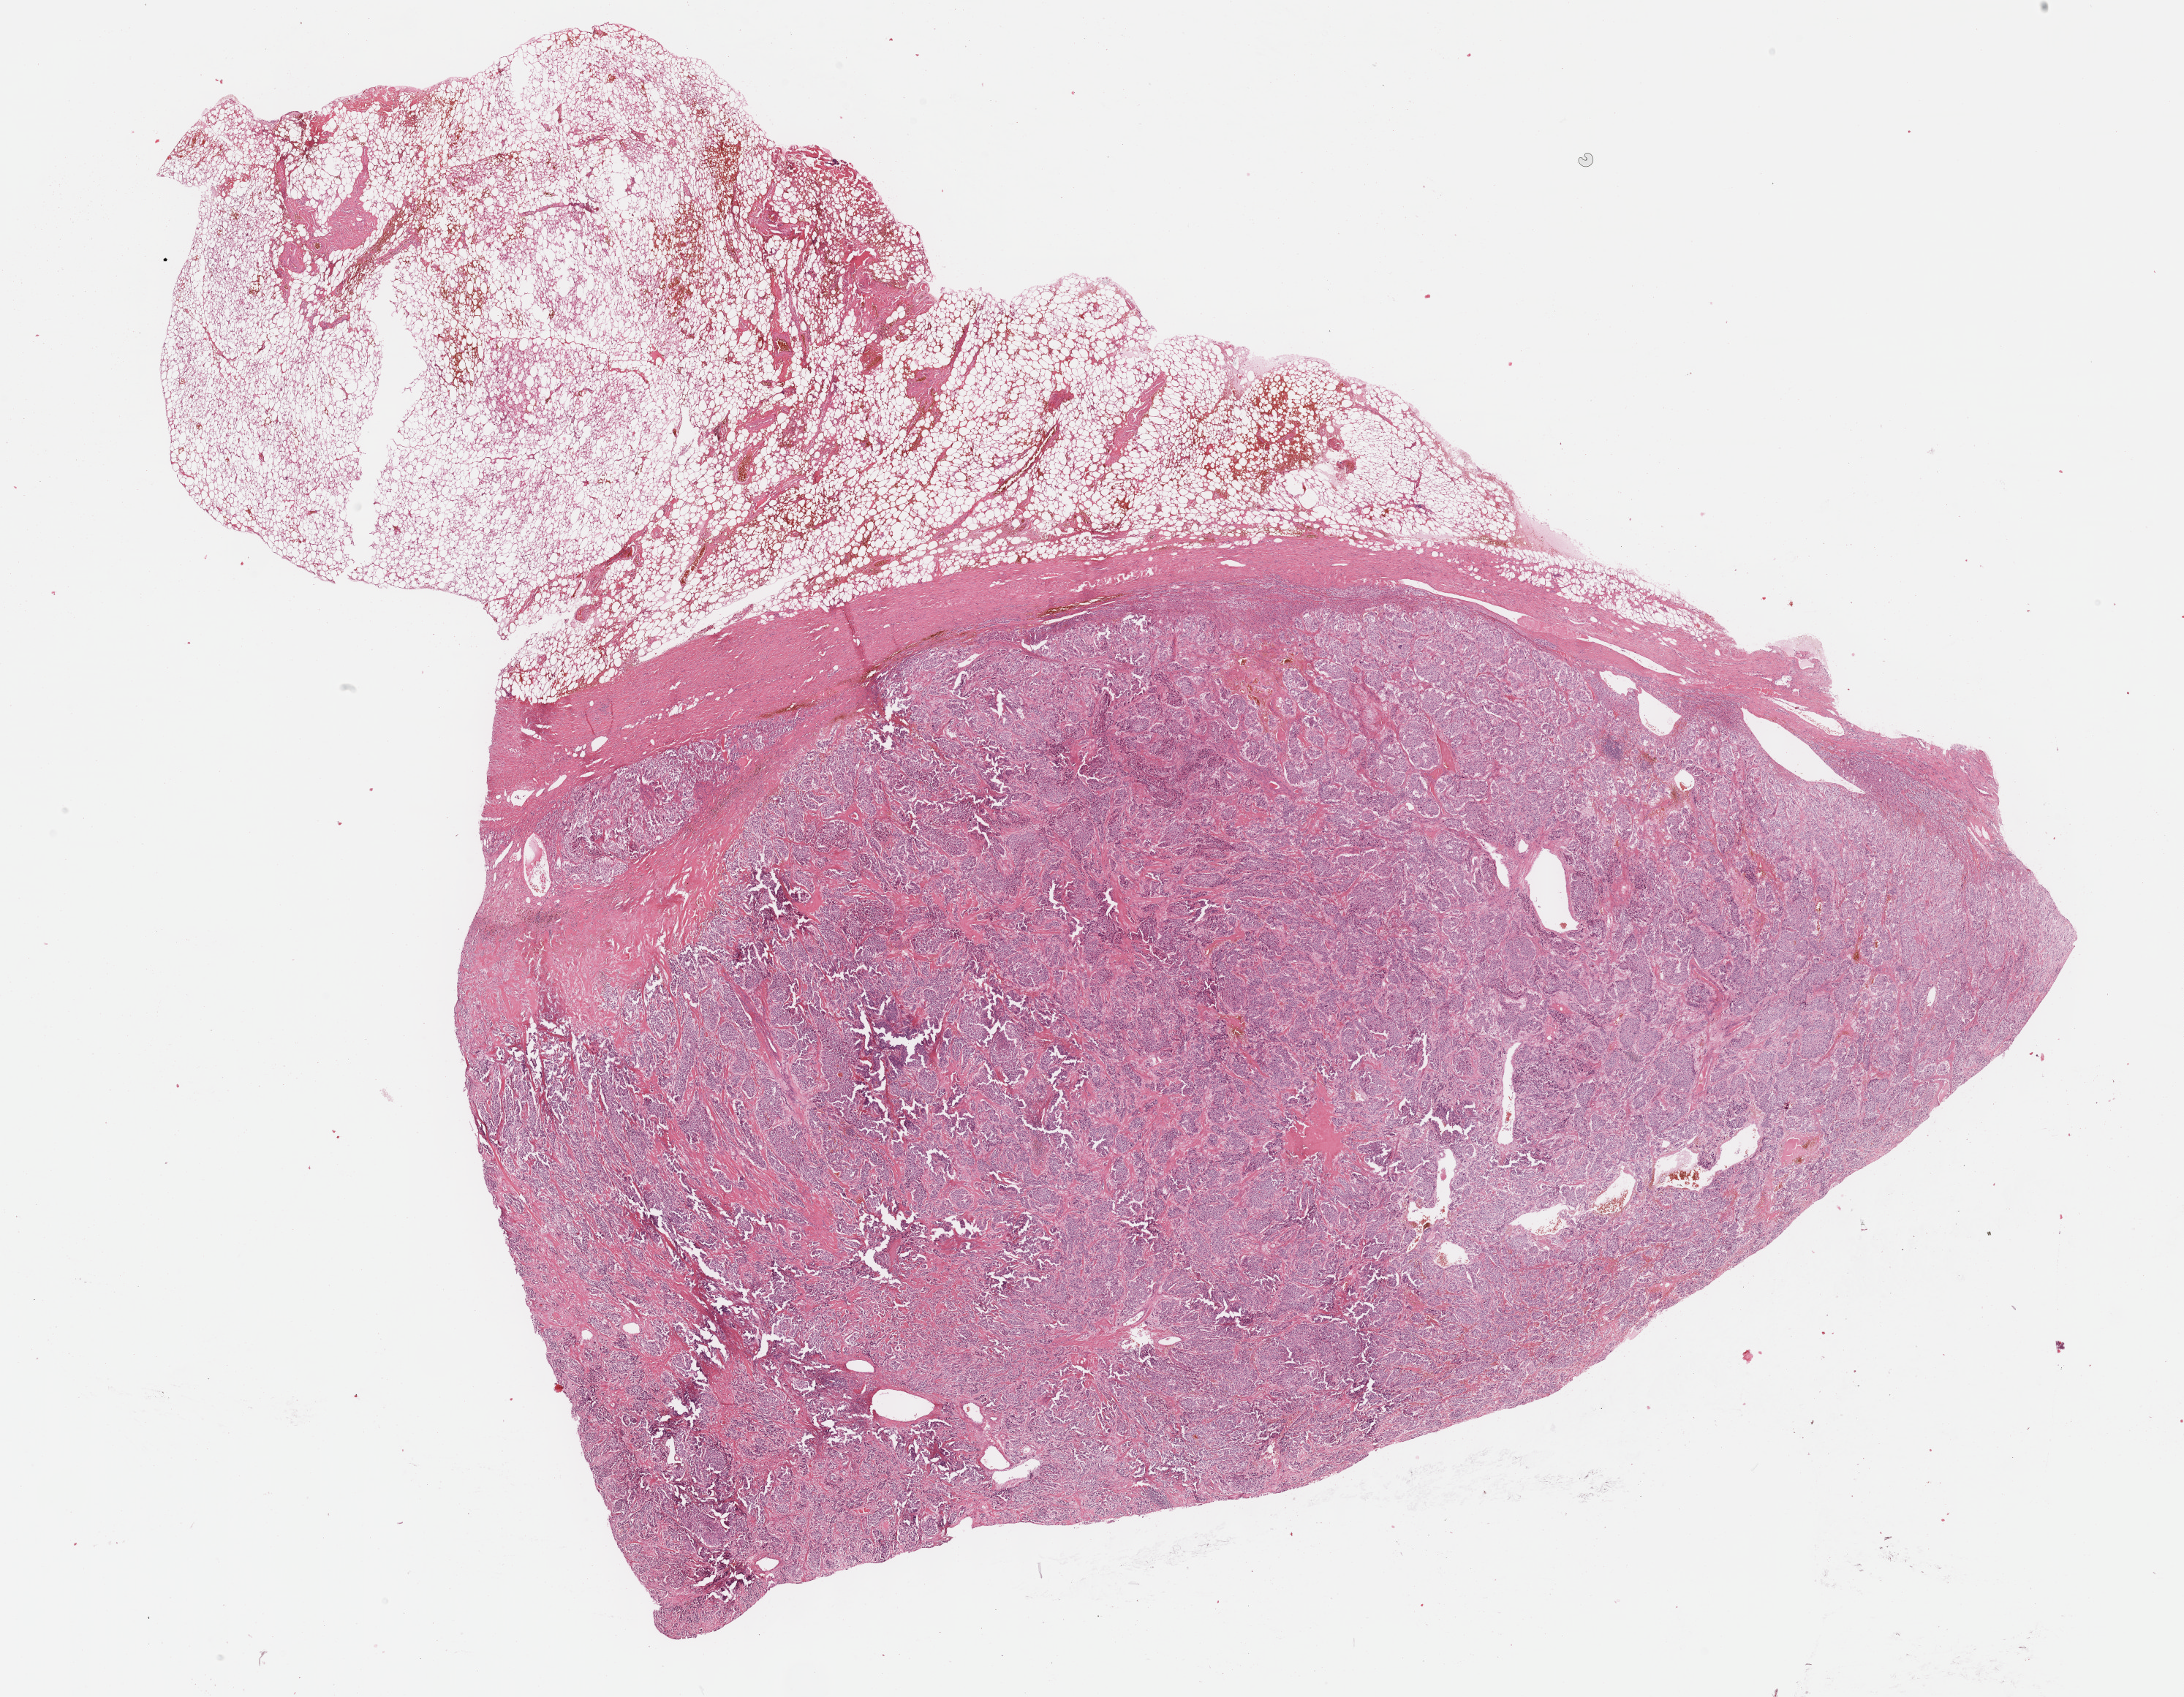
Digitized H&E tissue section (whole slide) — shown as a low-resolution overview of the whole scanned area (about 24.2 x 18.8 mm, from a 40x scan), FFPE section, primary tumour sample from the adrenal gland. Male, age 34 years at initial diagnosis.
• diagnosis: Pheochromocytoma, NOS
• laterality: left